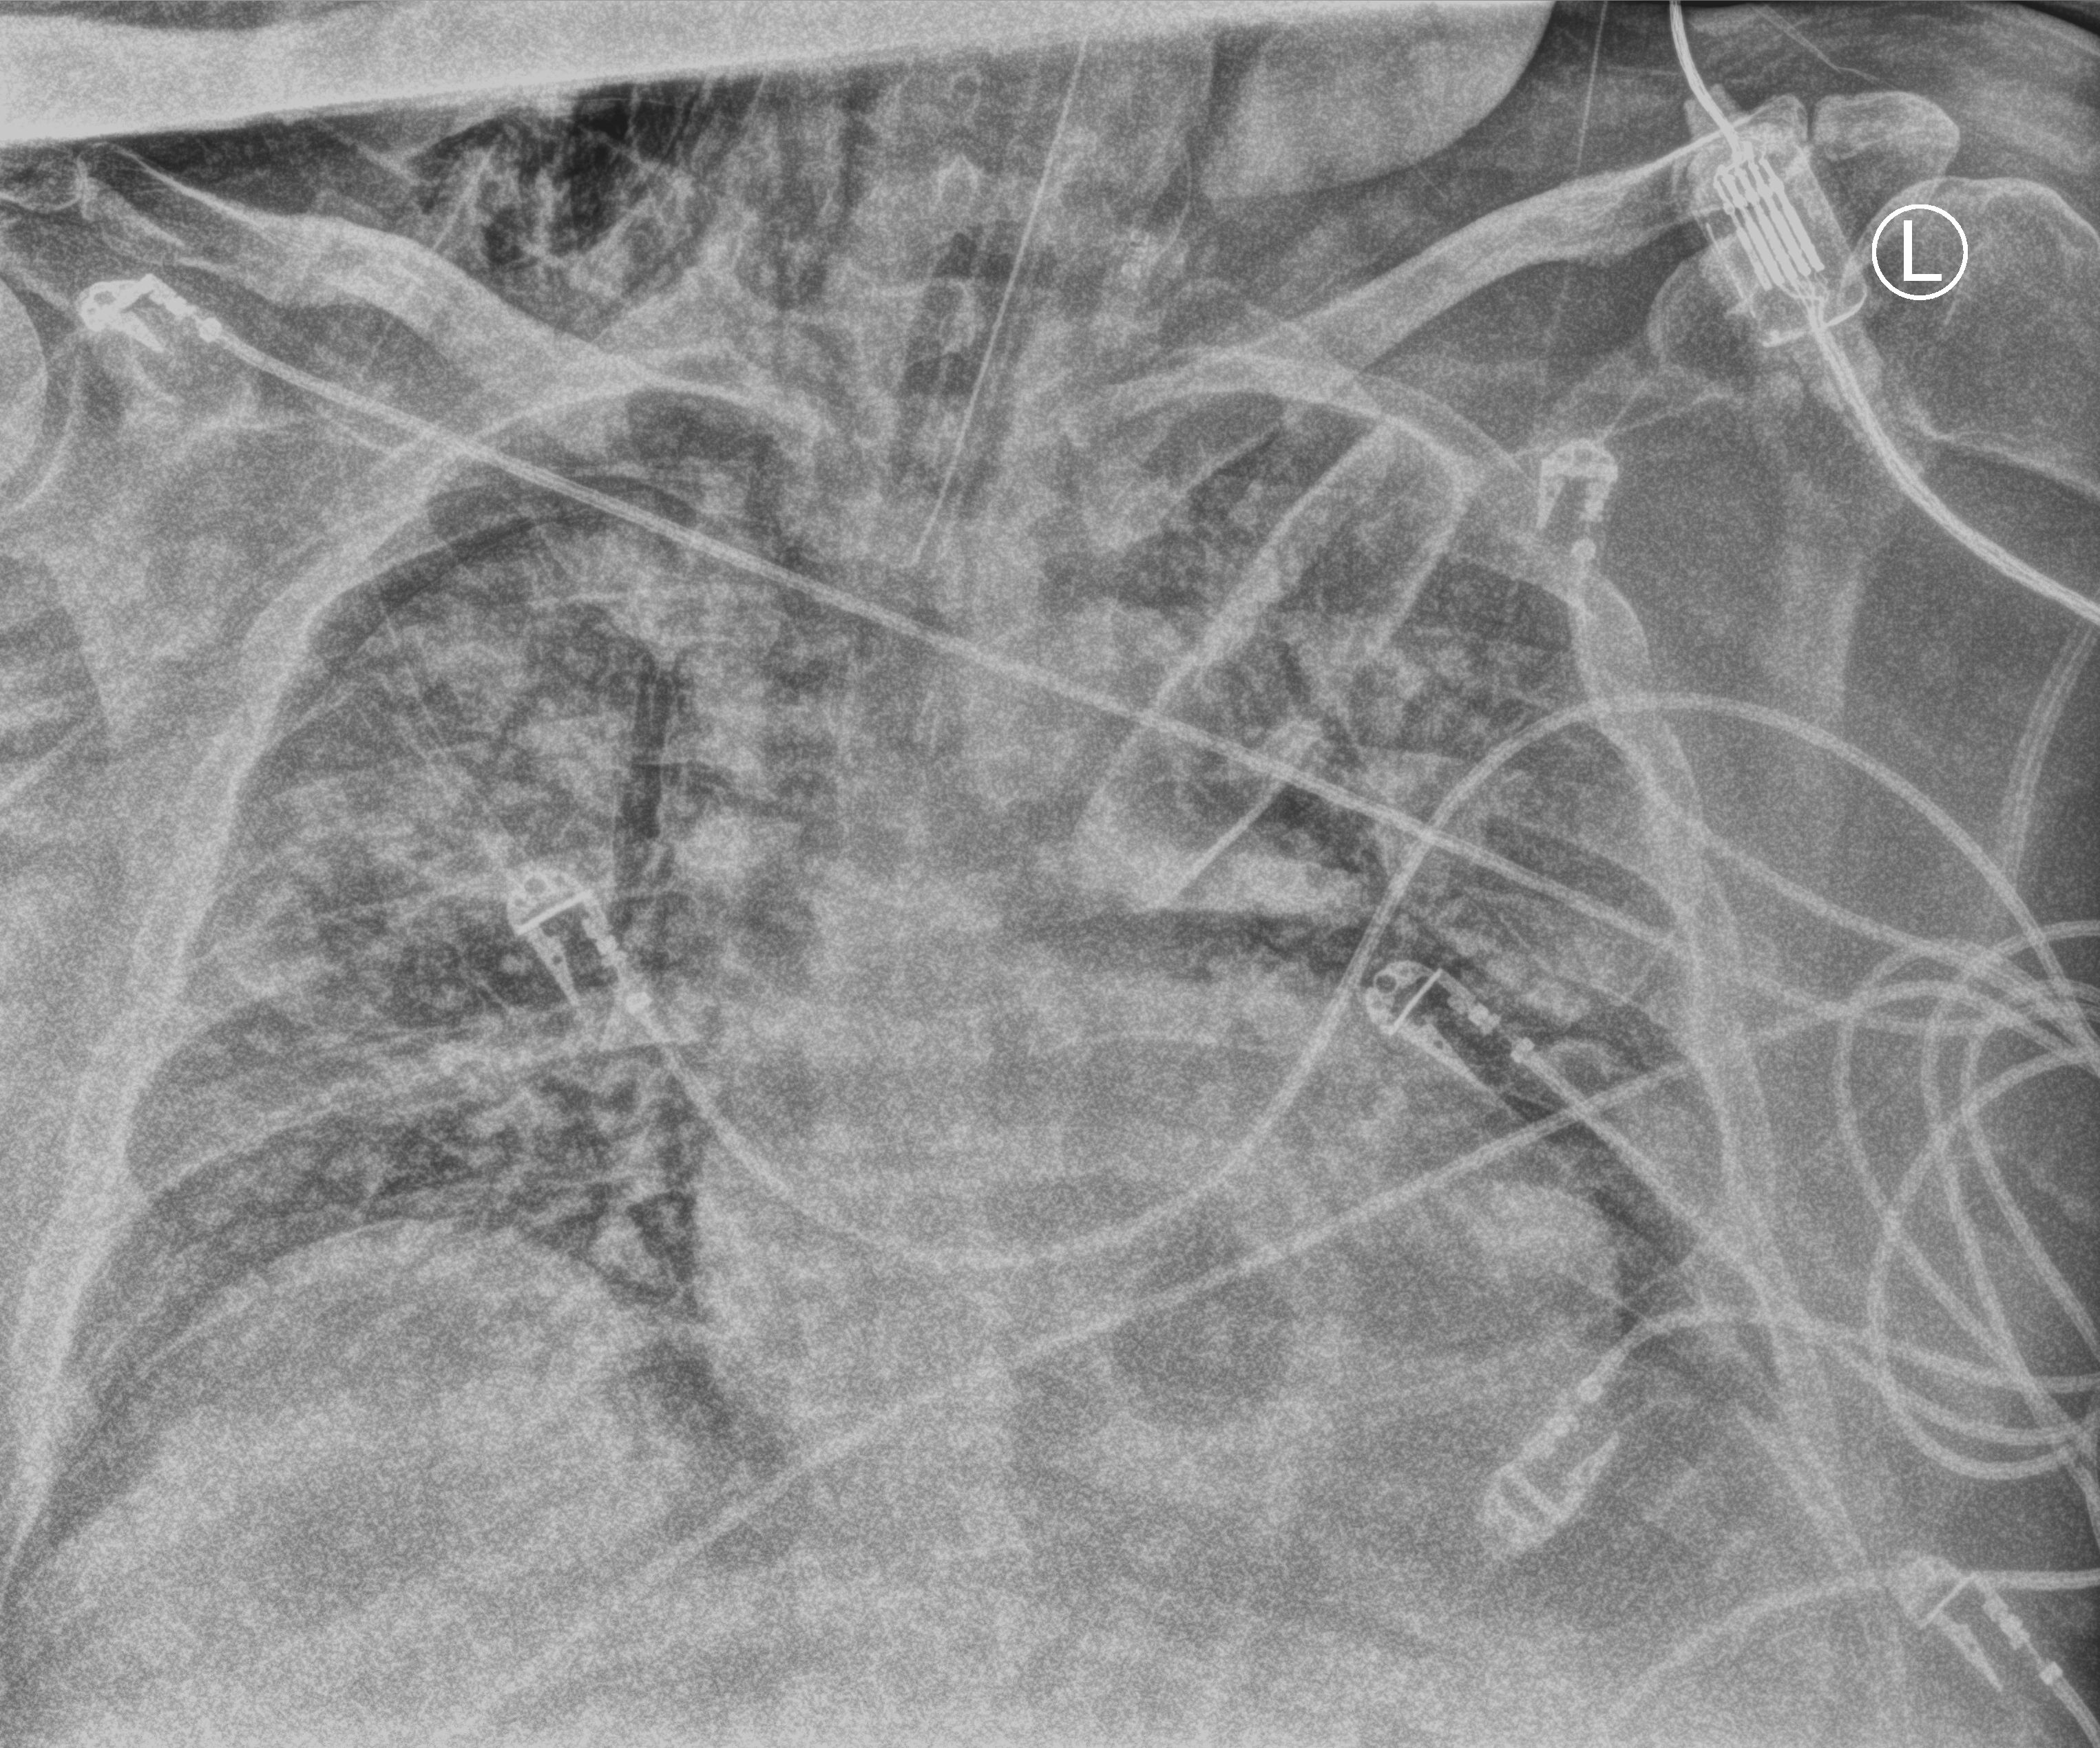
Portable chest radiograph; anteroposterior (AP) projection. Adult patient hospitalised with COVID-19, age 18–59 years.
Admission-level facts for this patient (not findings on this image; timing relative to this image not recorded): COPD (admission record): no.